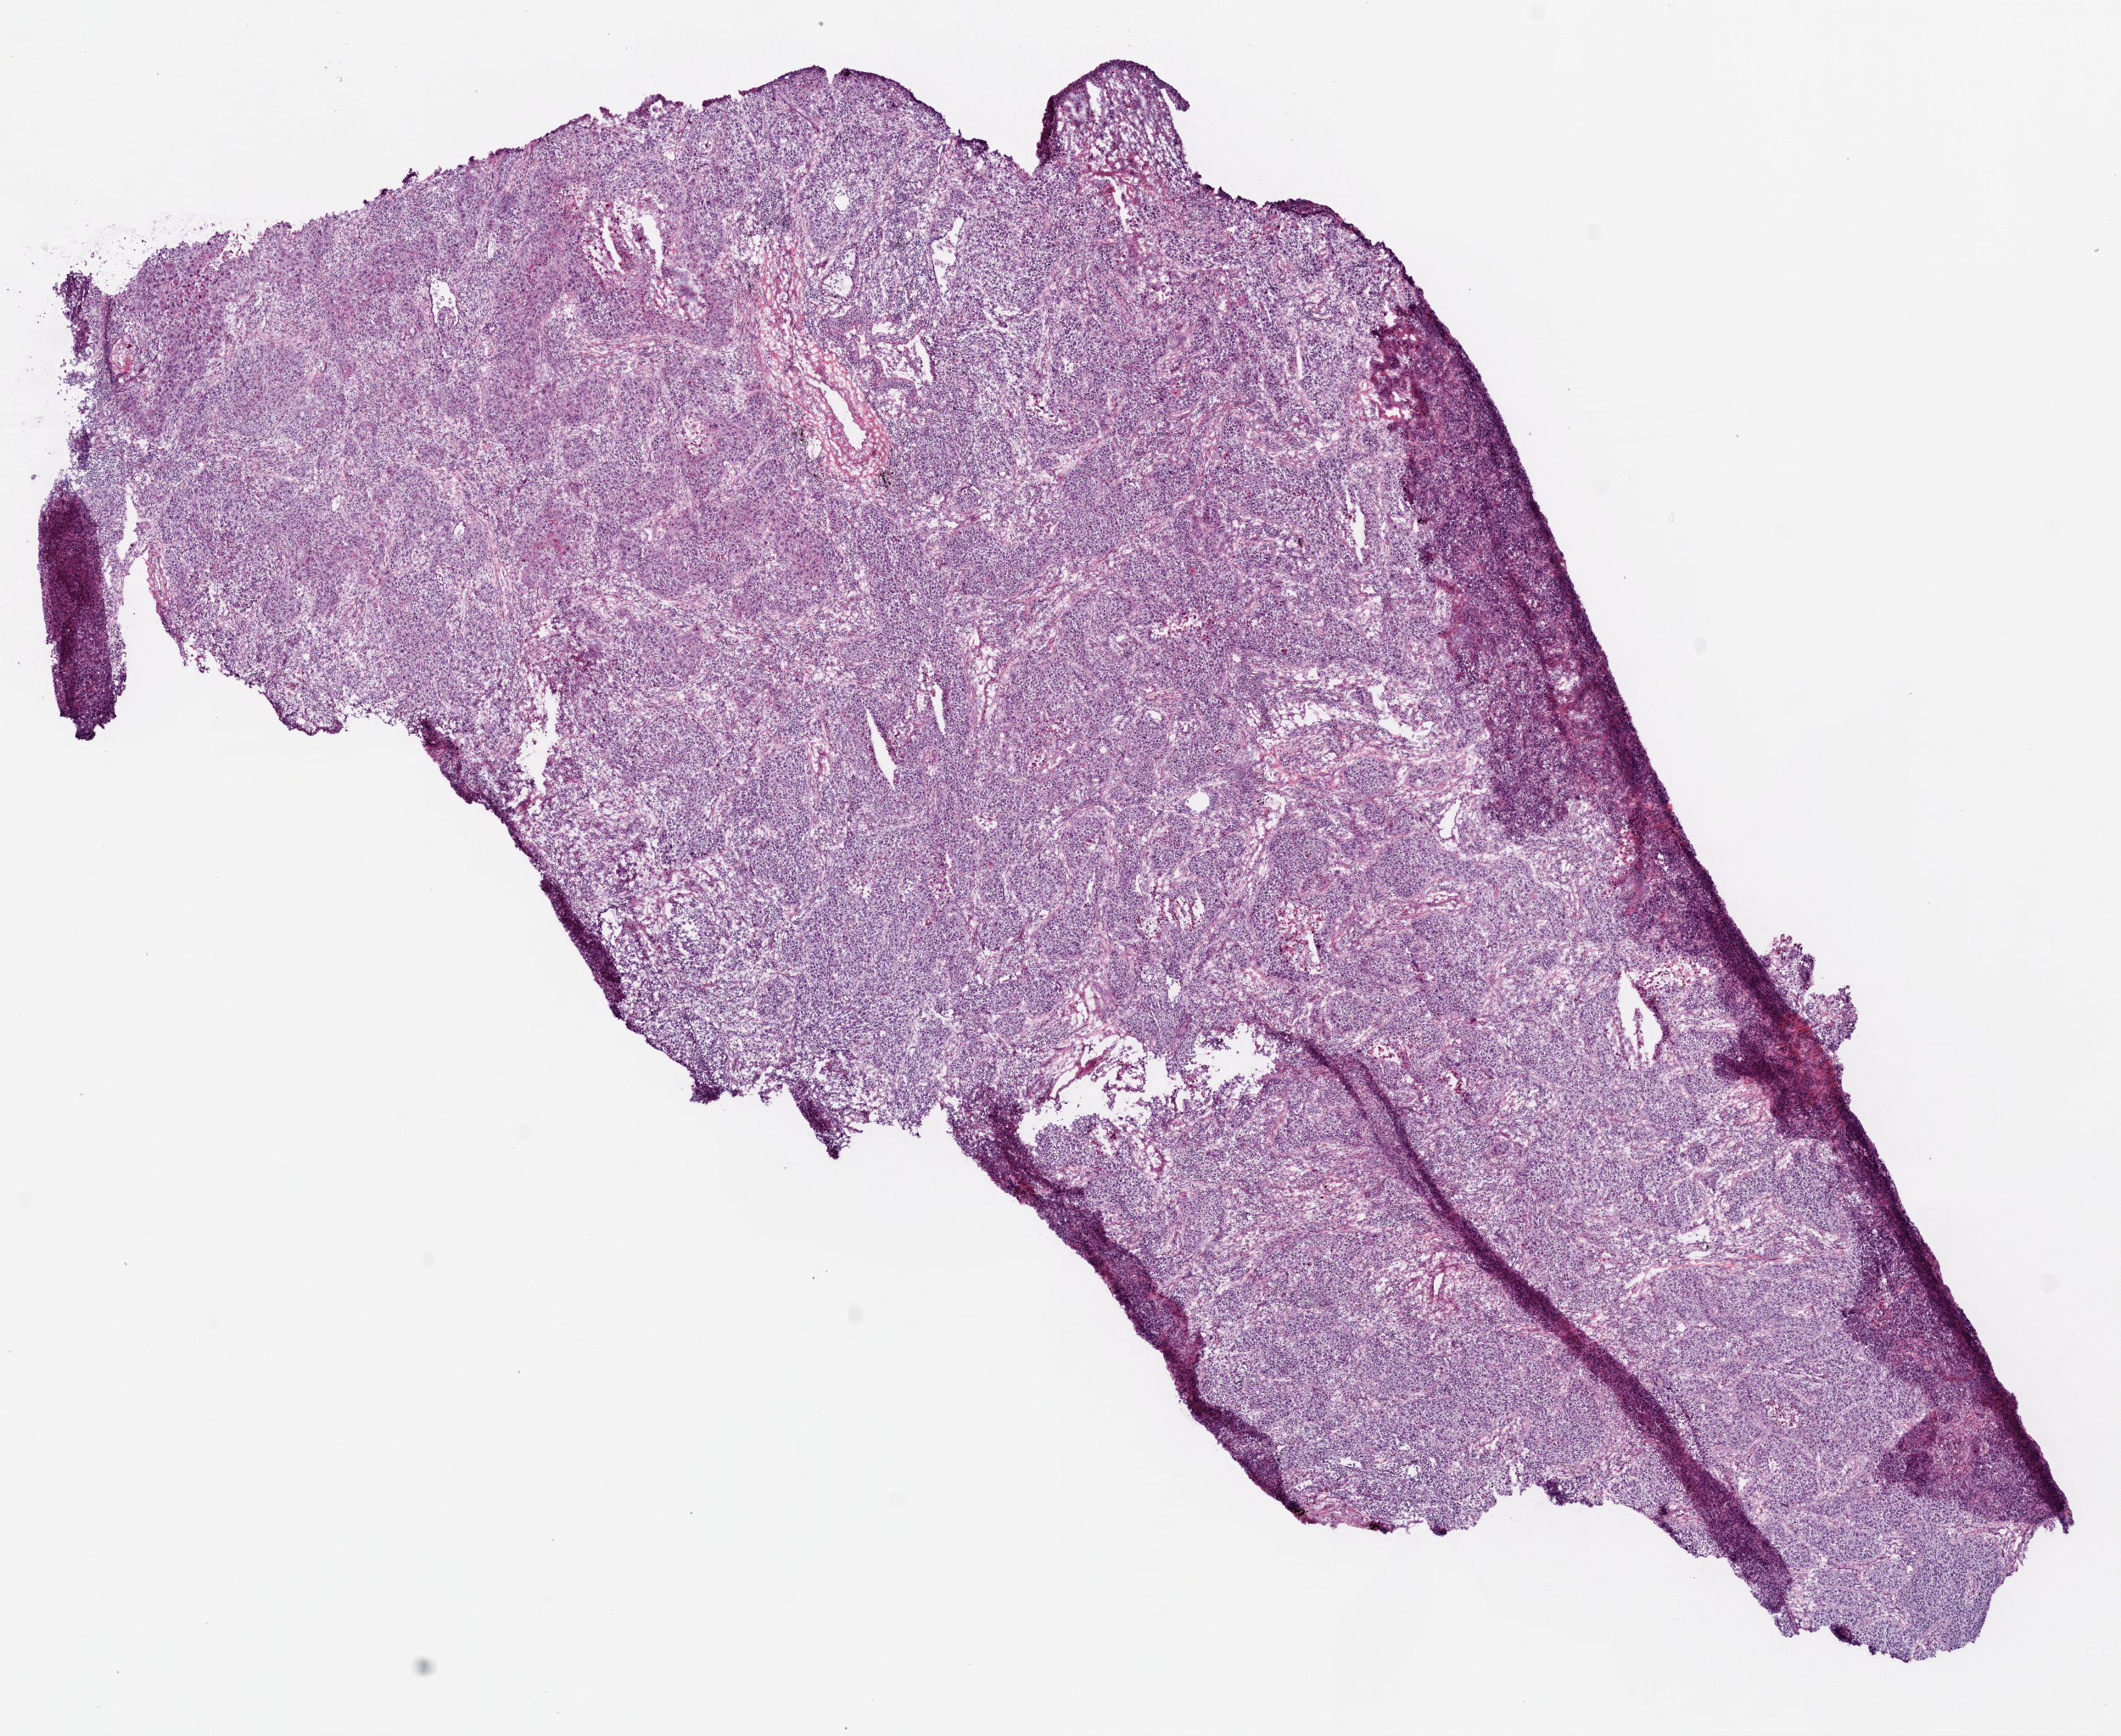
Whole-slide histology image, Hematoxylin and eosin (H&E) stained — a low-resolution overview of the entire scanned area, about 10.0 x 8.2 mm (acquisition: 20x scan); frozen section; sample: primary tumour, lung. Patient: male, age at initial diagnosis 69 years. Composition of this section per pathologist review: tumour cells 89%, tumour nuclei 60%, normal cells 1%, stromal cells 5%, necrosis 5%. Infiltration values recorded for this section: lymphocyte infiltration 30%, monocyte infiltration 3%, neutrophil infiltration 2%.
Diagnosis: Squamous cell carcinoma, NOS (lower lobe, lung). AJCC pathologic stage: IB (6th edition).